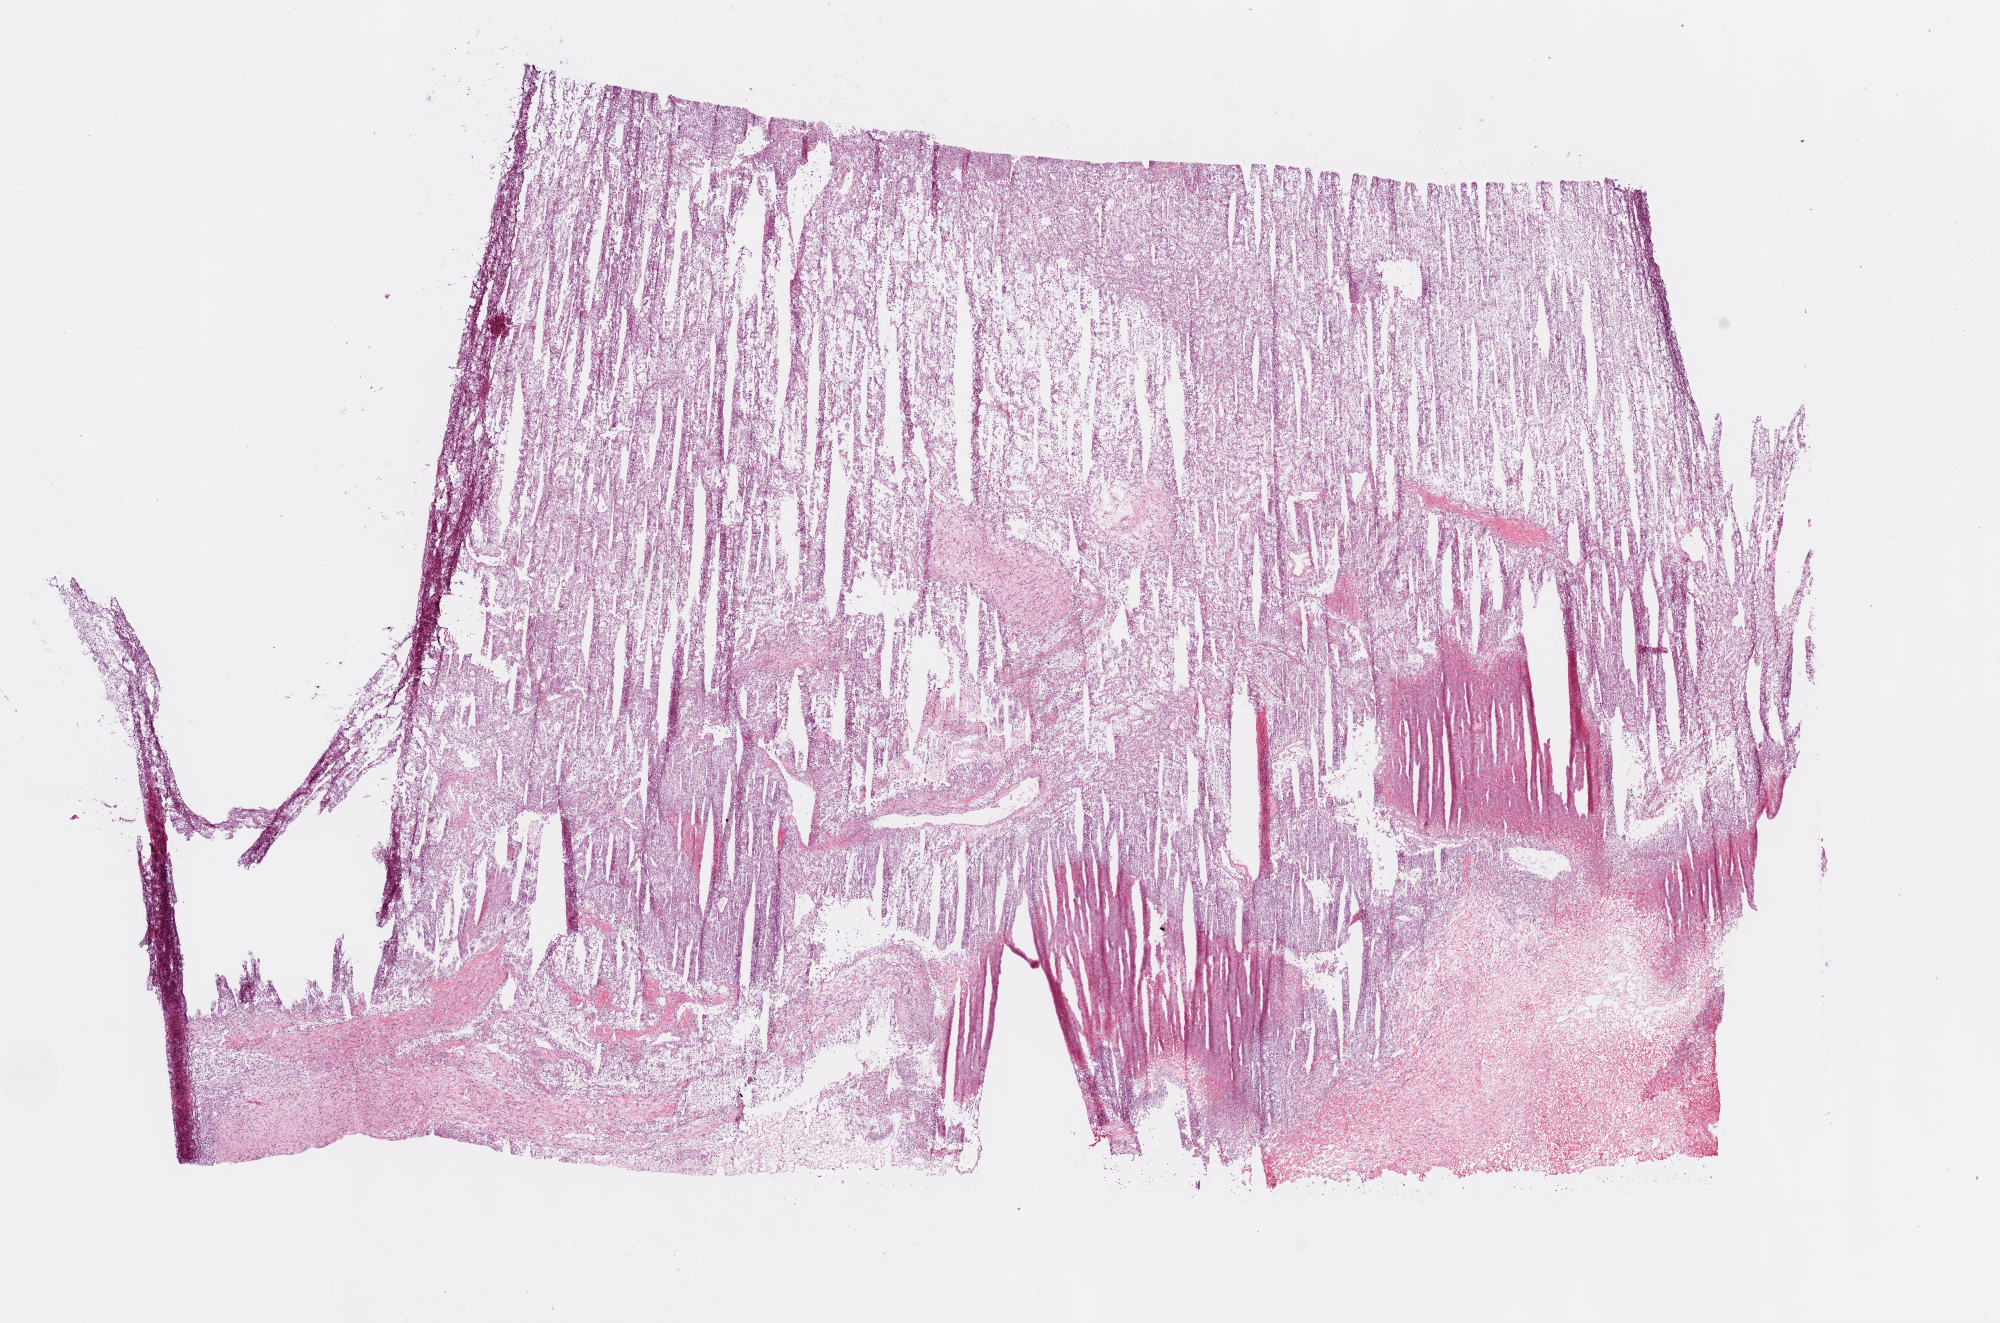
H&E whole-slide image, a low-resolution overview of the entire scanned area, about 16.0 x 10.6 mm (acquisition: 20x scan). Frozen section from the bottom of the tissue portion. Sample: primary tumour, kidney. Patient: male, age at initial diagnosis 56 years. Histologic grade: G4 (undifferentiated). Slide review estimates, as recorded: tumour cells 75%, tumour nuclei 85%, normal cells 0%, stromal cells 15%, necrosis 10%.
Diagnosis: Clear cell adenocarcinoma, NOS. AJCC pathologic stage: III (7th edition).